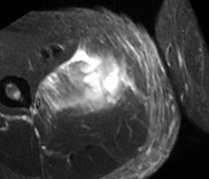
MRI of an extremity soft-tissue mass, one axial slice; slice 31 of 89 in the series (ordered by position); STIR; MR volume resampled by the dataset authors to the PET/CT grid (not the native acquisition matrix); 3.27 mm slice thickness; 209 × 179 image matrix. Male patient. Case-level facts recorded for this patient, not image findings: histological type: undifferentiated - pleiomorphic; grade: high; site of the primary tumour: right thigh.
Outlined on this slice (expert contour drawn on MRI and transferred to this co-registered scan by the dataset authors):
- gross tumour volume including surrounding oedema: bounding box [x1, y1, x2, y2] px = [30, 47, 127, 118]
- gross tumour volume (mass): [66, 55, 127, 115]